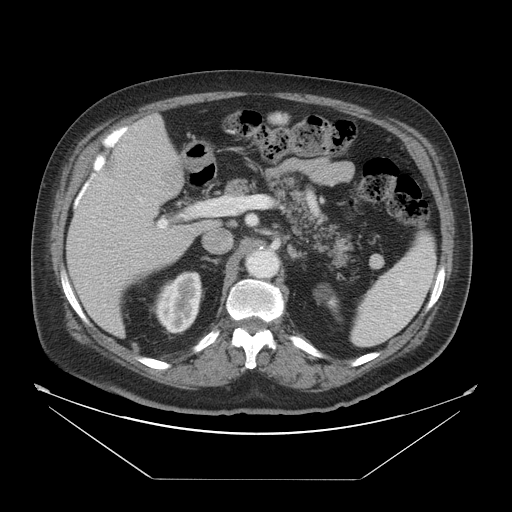
Contrast-enhanced abdominal CT, one axial slice; position 28 of 45 along the scan axis; reconstruction kernel STANDARD; 120 kVp; soft-tissue window (W 400 / L 40 HU); 5 mm slice thickness; 512 × 512 image matrix, field of view 463 × 463 mm. Male patient, age 87 years. From the clinical record (not read from this slice): diagnosis: colorectal cancer liver metastases, imaged before liver resection; multiple liver metastases: no; largest metastasis: 4.5 cm; disease in both lobes: yes.
Annotated regions visible in this slice (outlined manually by an expert reader):
- liver: box from (x=67, y=114) to (x=218, y=338) px
- planned liver remnant (the part of the liver to remain after resection): (x=124, y=114)–(x=177, y=156)
- portal vein (with intrahepatic branches): (x=133, y=191)–(x=208, y=227)
- liver metastasis: (x=161, y=163)–(x=184, y=193)
- liver metastasis: (x=102, y=153)–(x=121, y=184)